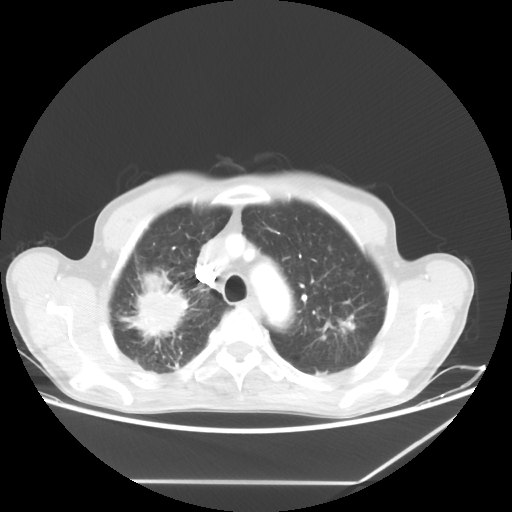
Chest CT, one axial slice. Slice 50 of 65 in the series (ordered by position). Reconstruction kernel STANDARD. 80 kVp. Lung window (W 1500 / L -600 HU). 5 mm slice thickness. 512 × 512 image matrix, field of view 397 × 397 mm. Patient: male, 68 years. From the clinical record (not read from this slice): clinical TNM (as recorded): T3 N3 M0.
Annotated regions visible in this slice (rectangle marked by the reading radiologist):
- lung tumour (recorded histology: adenocarcinoma): bounding box <130,262,195,349> (left, top, right, bottom; pixels)